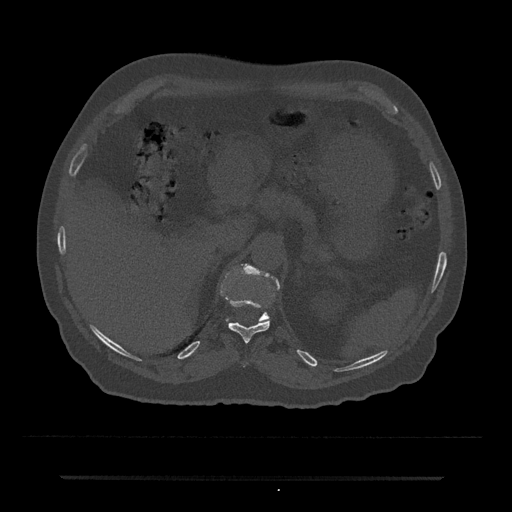
CT including the spine, one axial slice. Position 169 of 797 along the scan axis. Bone window (W 1800 / L 400 HU). 512 × 512 image matrix, field of view 437 × 437 mm. Male patient, age 69 years. Case-level facts recorded for this patient, not image findings: primary cancer: prostate.
Outlined on this slice (semi-automatically segmented with operator editing):
- T11 vertebra: bounding box <225,296,270,343> (left, top, right, bottom; pixels)
- T12 vertebra: <239,266,280,321>